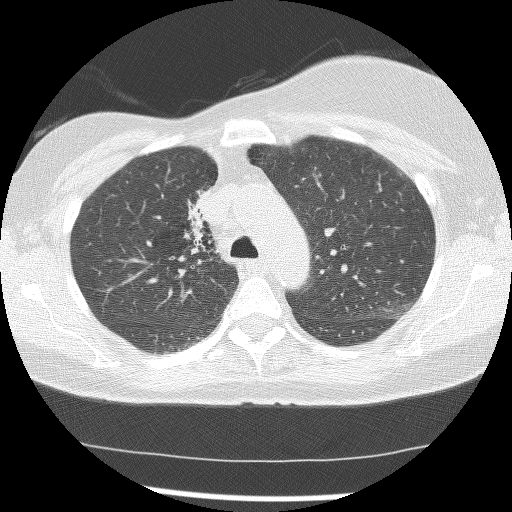
Axial slice from a low-dose chest CT screening exam, baseline annual screen, lung window (W 1500 / L -600 HU), 2.5 mm slice thickness, slice 44 of 172 in the series, 512 × 512 image matrix, field of view 315 × 315 mm. Female, age 56 years at enrolment. Current smoker at enrolment.
Lesion marked by an expert reader, box from (x=164, y=182) to (x=221, y=269) px. The screening reader recorded 2 non-calcified nodules or masses ≥4 mm on this exam (right lower lobe, right middle lobe); which of them this box marks is not recorded. Official screen result: positive, change unspecified: nodule(s) >= 4 mm or enlarging nodule(s), mass(es), or other non-specific abnormalities suspicious for lung cancer. Later outcome: lung cancer diagnosed 1185 days after this screen — adenocarcinoma, NOS, right upper lobe, stage IIIB (AJCC 6th edition), 8 mm at pathology.